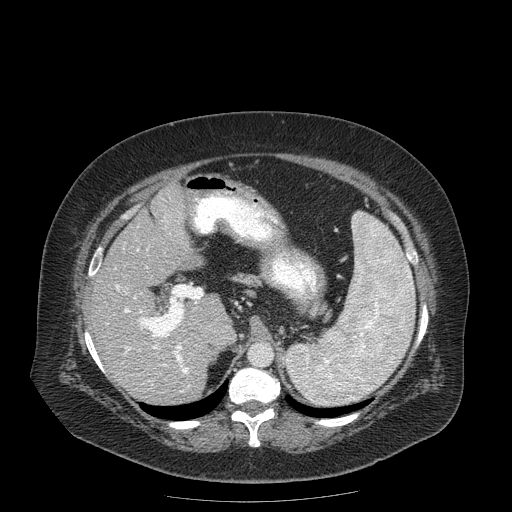
Contrast-enhanced abdominal CT (liver protocol), one axial slice. Position 113 of 204 along the scan axis. Reconstruction kernel STANDARD. 120 kVp. Soft-tissue window (W 400 / L 40 HU). 2.5 mm slice thickness. 512 × 512 image matrix, field of view 440 × 440 mm. From the clinical record (not read from this slice): diagnosis: hepatocellular carcinoma (patient treated with transarterial chemoembolisation; whether this scan precedes or follows treatment is not stated here); TNM stage (as recorded): Stage-IIIB; Child-Pugh class: A; tumour nodularity: uninodular.
Structures marked on this image (semi-automatically segmented with operator editing):
- liver parenchyma outside the tumour (the mass and vessels are separate outlines, so this box may not span the whole liver): bounding box [x1, y1, x2, y2] px = [90, 182, 234, 404]
- liver vessels: [115, 249, 197, 393]